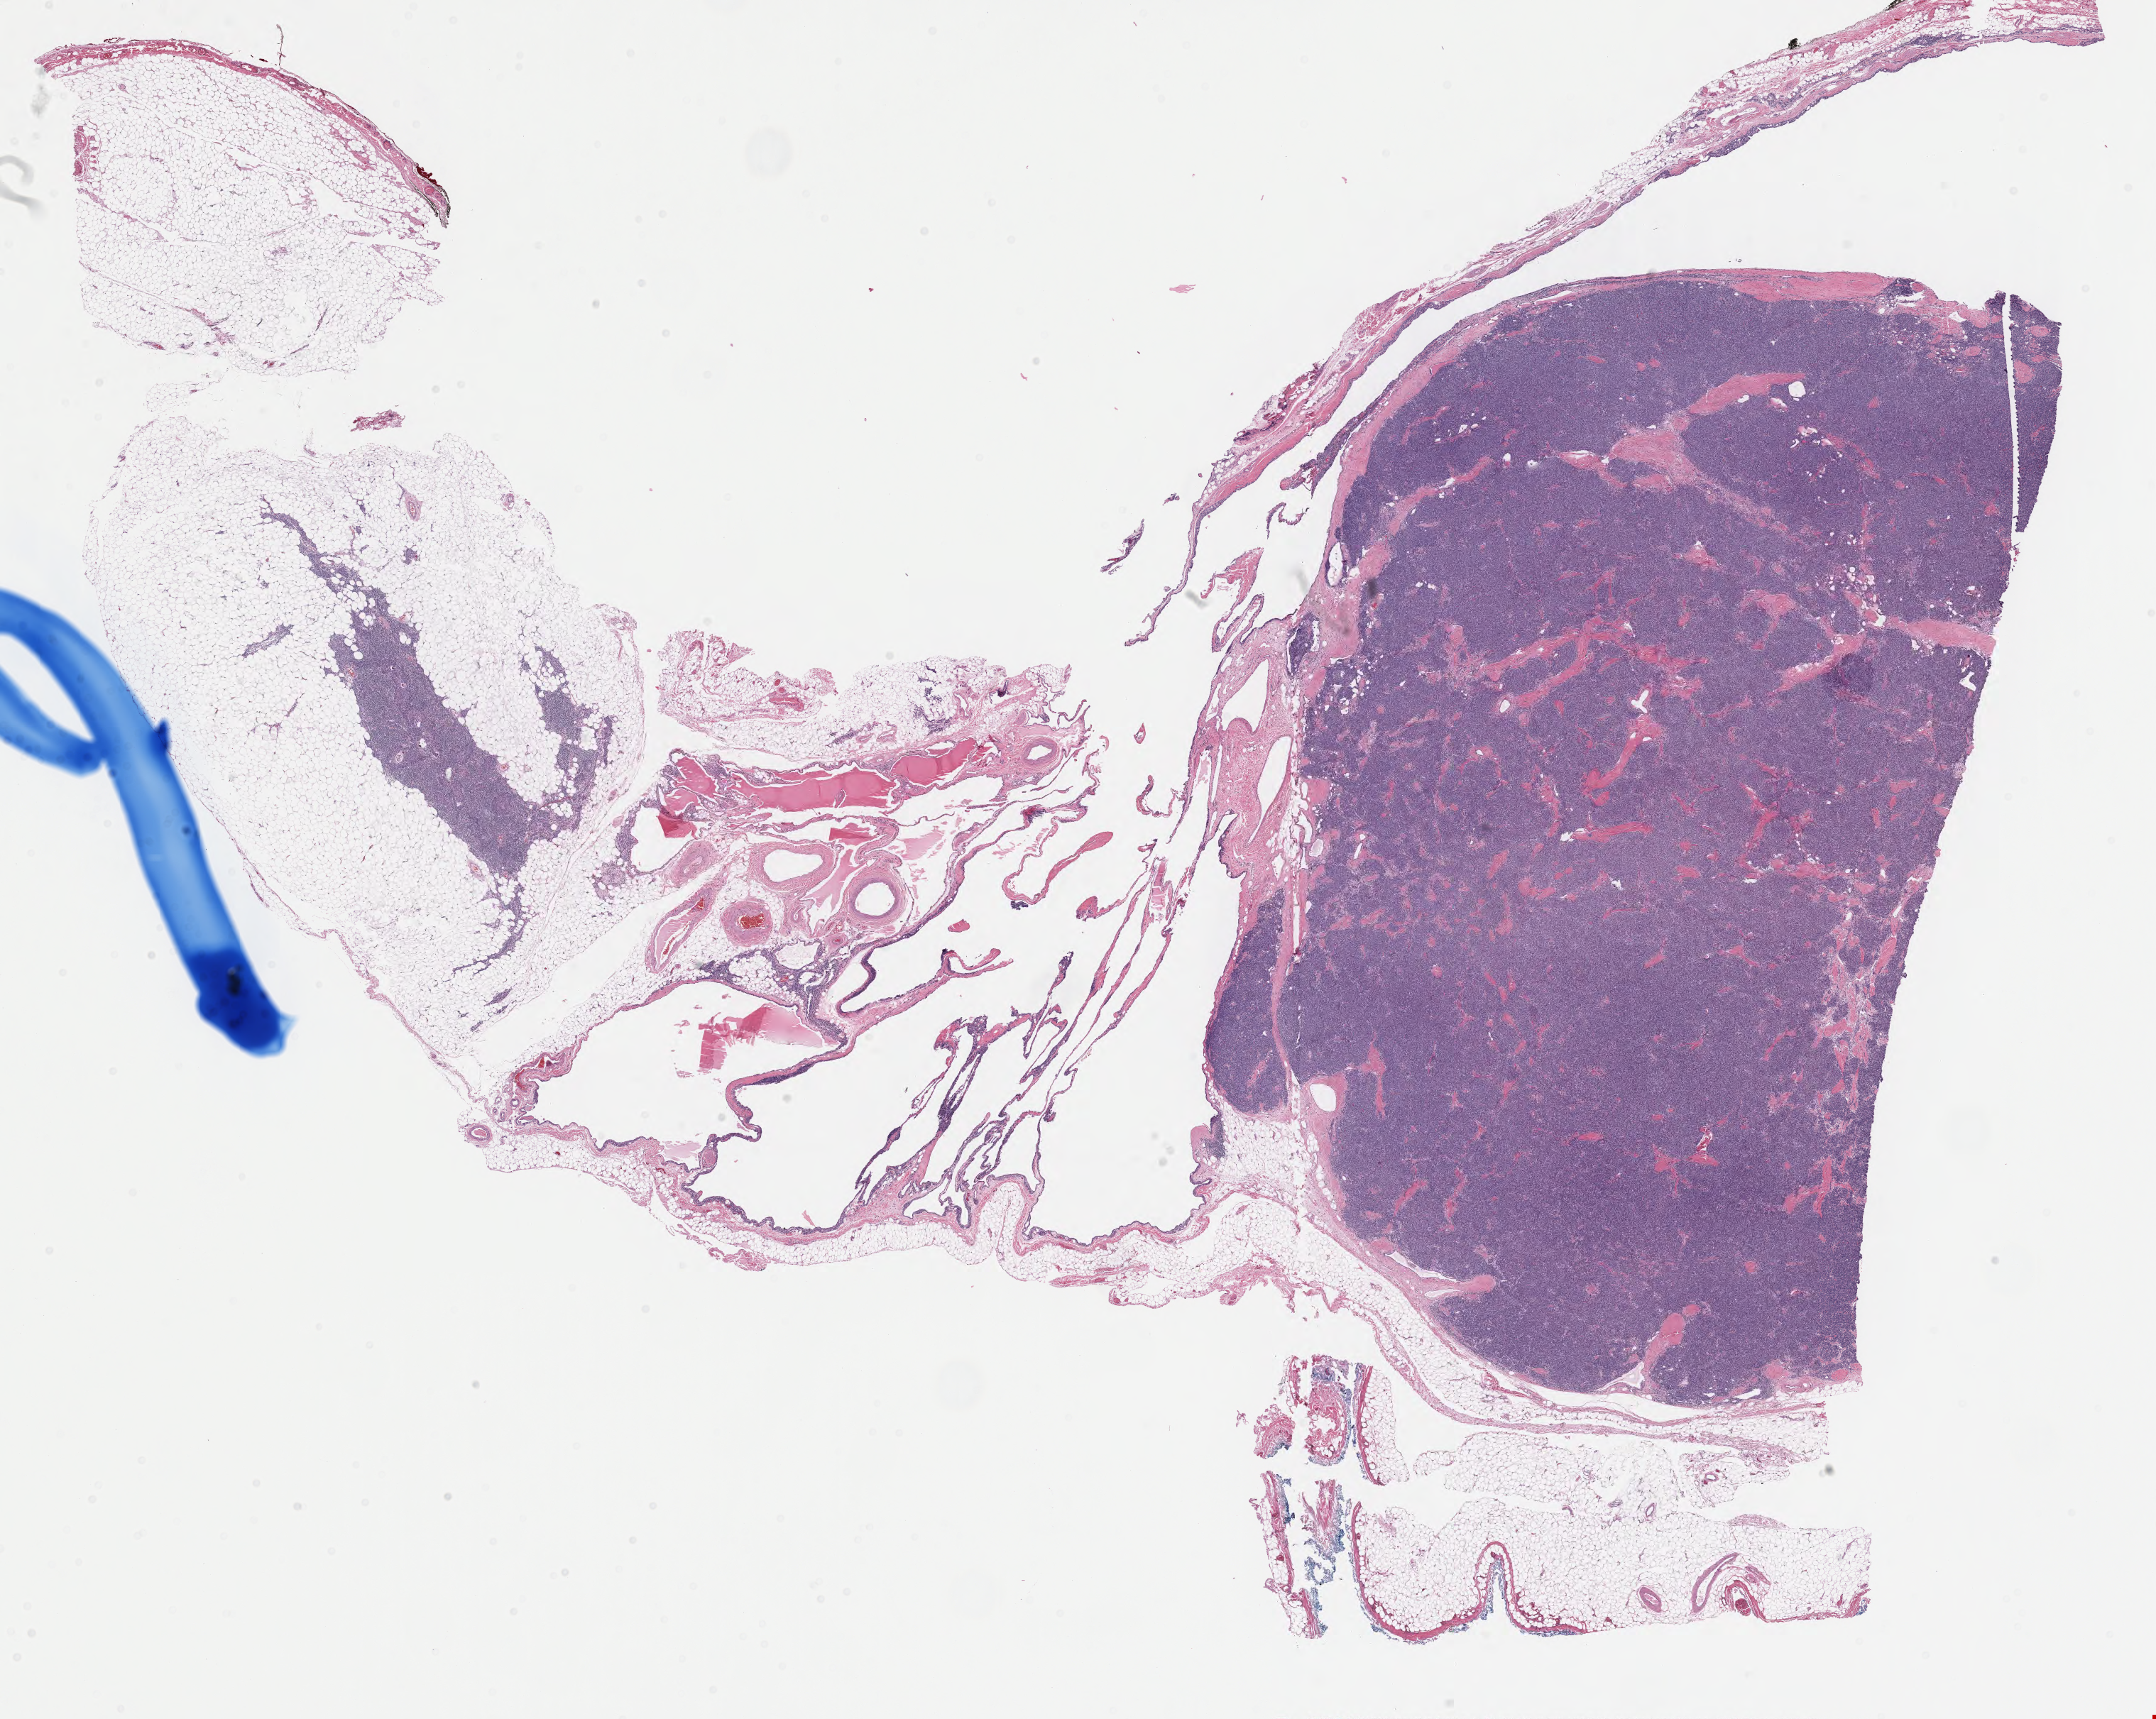
H&E whole-slide image, low-resolution overview of the scanned area, about 24.1 x 19.2 mm (slide scanned at 40x). Formalin-fixed paraffin-embedded (FFPE) diagnostic section. Sample: primary tumour, thymus. Patient: male, age at initial diagnosis 52 years.
Pathologic diagnosis: Thymoma, type A, malignant.